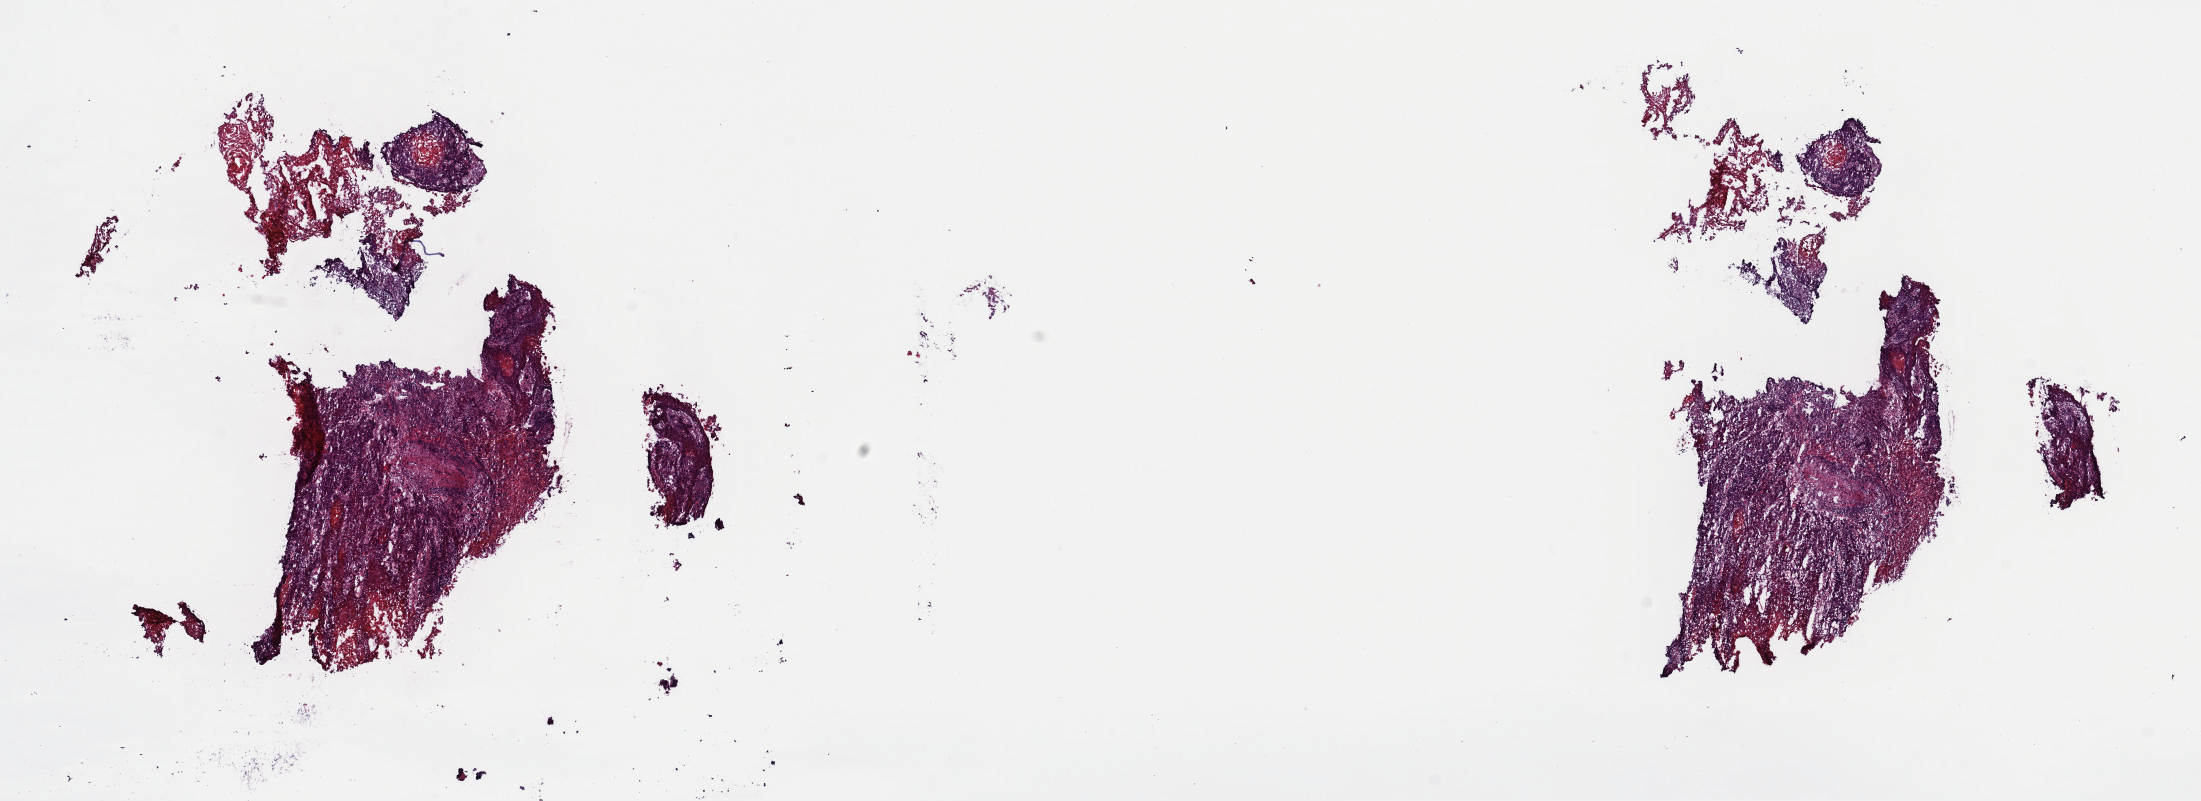
H&E-stained whole-slide image, shown as a low-resolution overview of the whole scanned area (about 17.4 x 6.3 mm, from a 40x scan), frozen section from the top of the tissue portion, primary tumour sample from the head and neck. Patient: male, age at initial diagnosis 65 years. Histologic grade: G2 (moderately differentiated). Slide review estimates, as recorded: tumour cells 60%, tumour nuclei 70%, normal cells 0%, stromal cells 20%, necrosis 20%. Inflammatory infiltration, as recorded: lymphocyte infiltration 2%, monocyte infiltration 0%, neutrophil infiltration 0%.
TNM: T4a N1 M0. Diagnosis: Squamous cell carcinoma, NOS (mouth, NOS). Laterality: right. AJCC pathologic stage: IVA (7th edition).